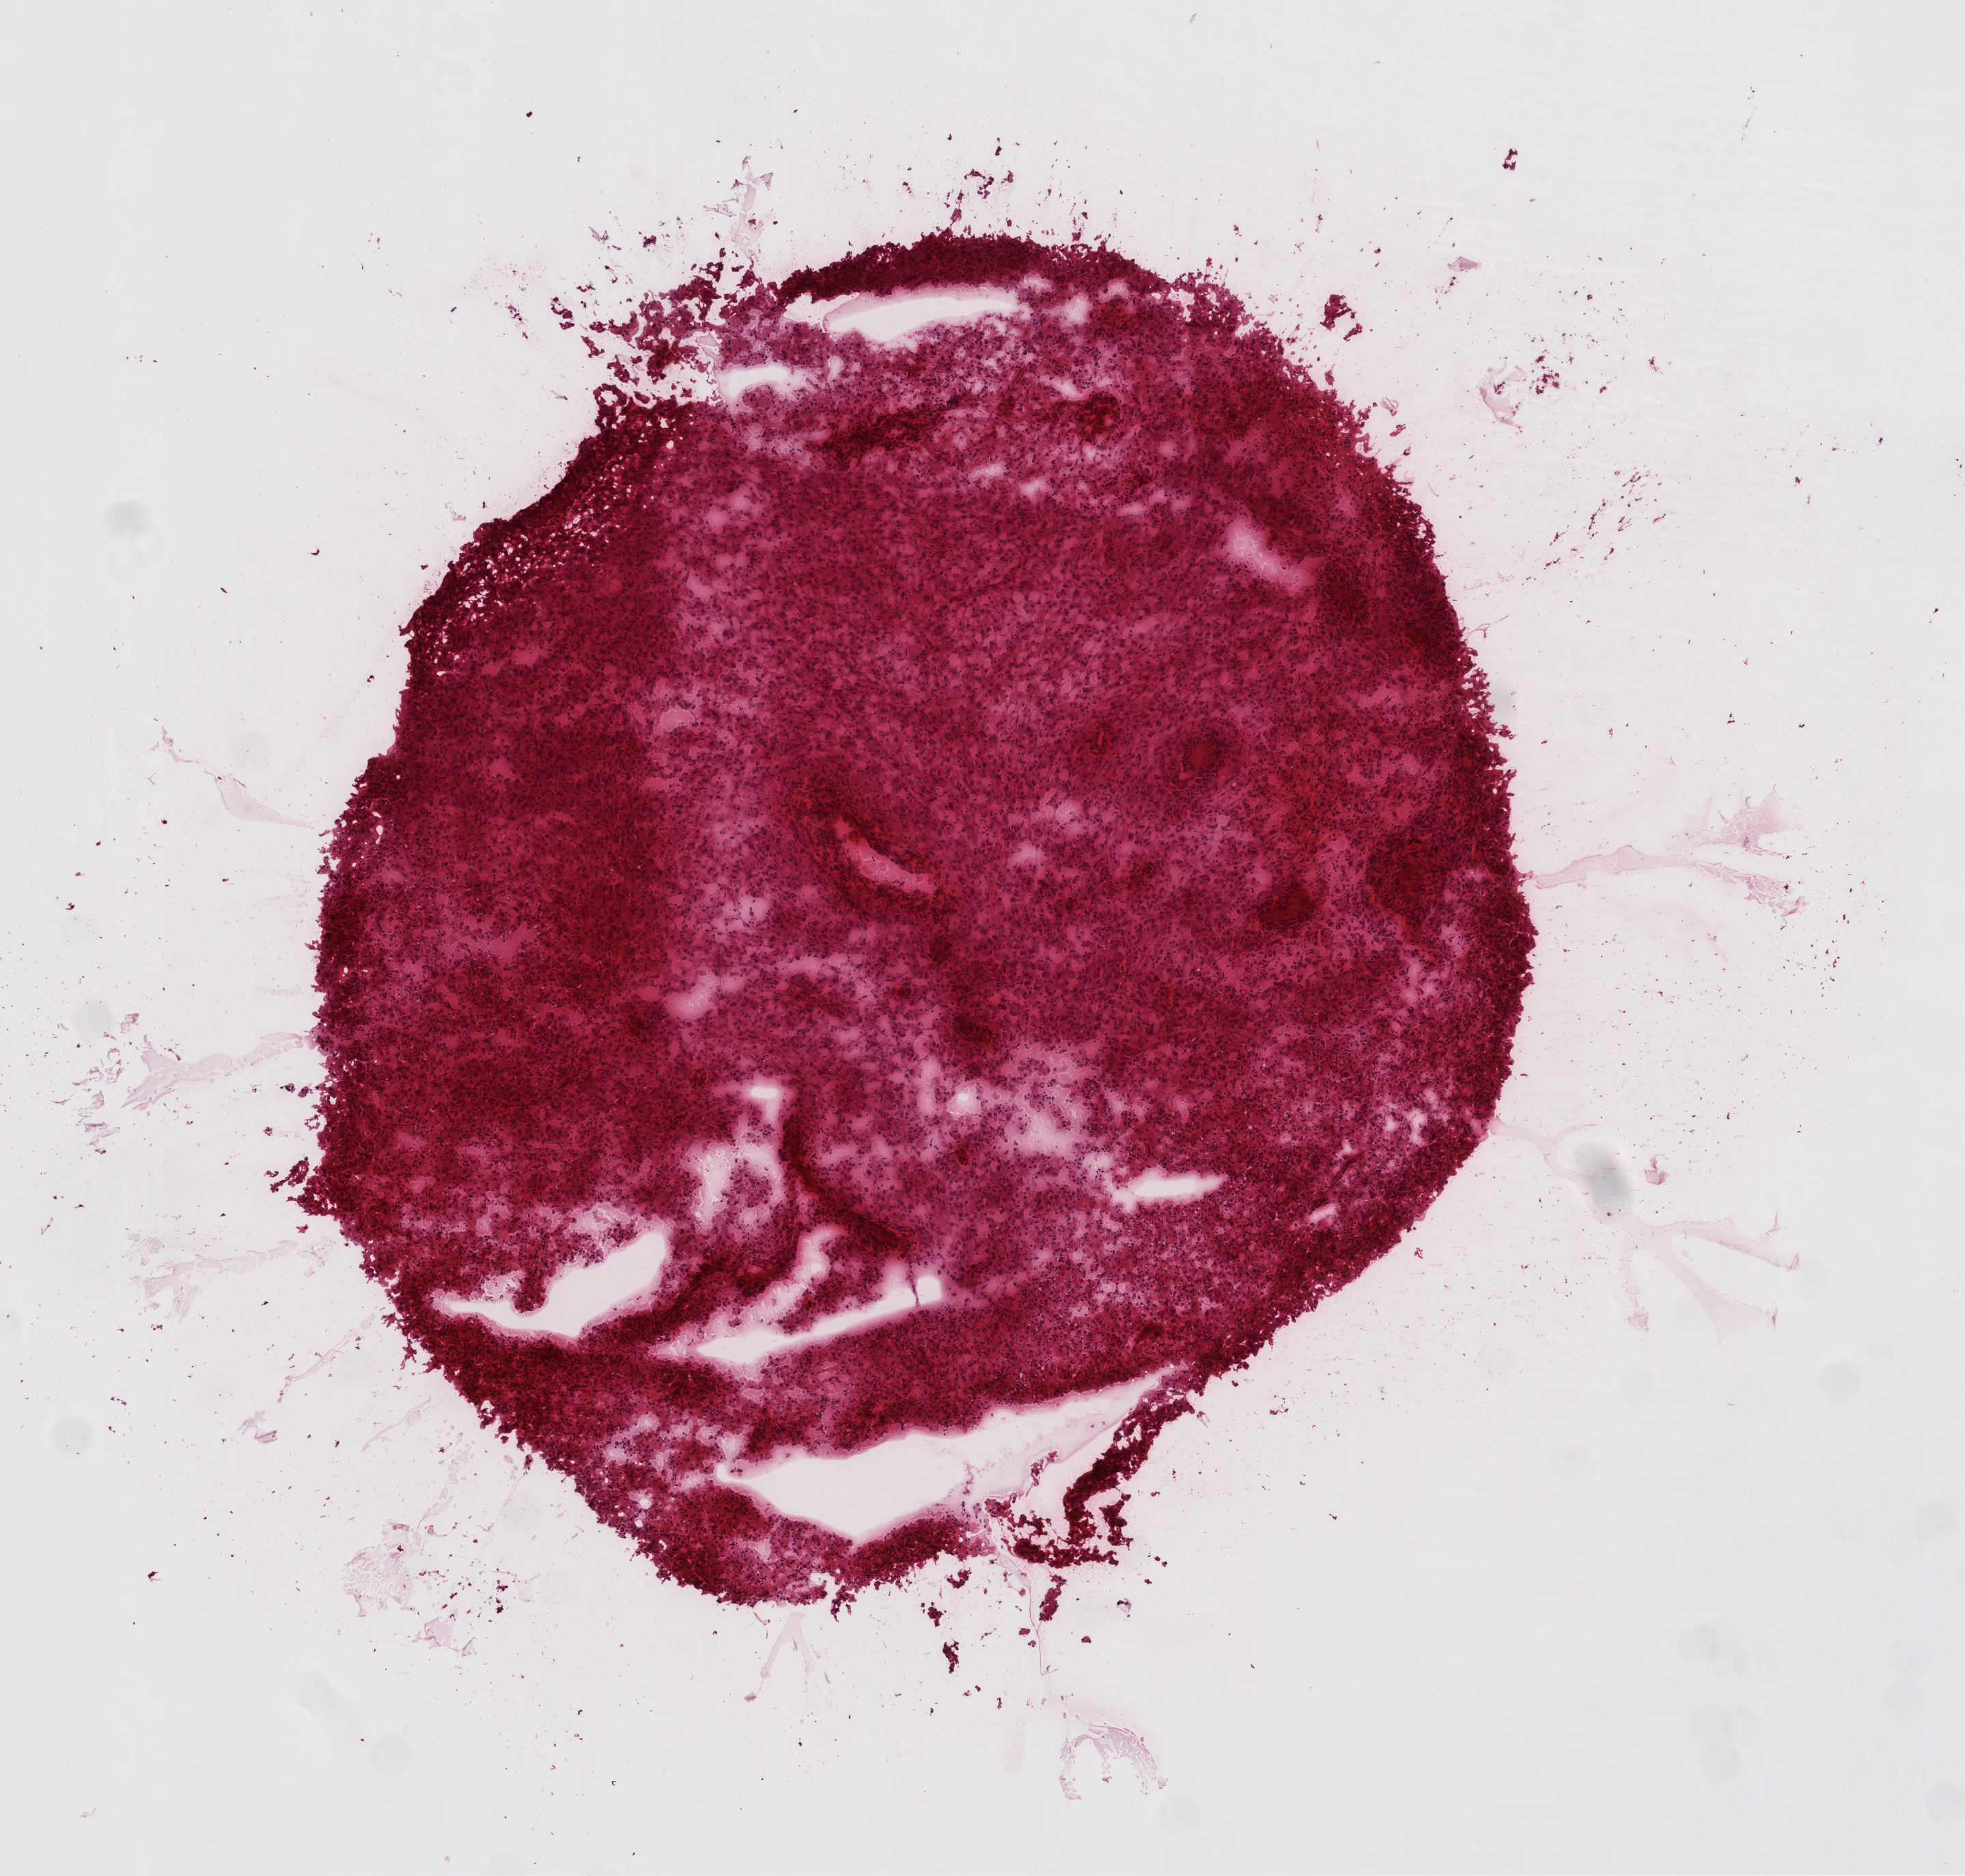
Digitized H&E-stained tissue section (whole slide) — shown as a low-resolution overview of the whole scanned area (about 5.8 x 5.5 mm, from a 20x scan). Frozen section from the top of the tissue portion. Brain, primary tumour sample. Female, age 48 years at initial diagnosis. Slide review estimates, as recorded: tumour cells 100%, tumour nuclei 100%, normal cells 0%, stromal cells 0%, necrosis 0%.
Pathologic diagnosis: Glioblastoma.